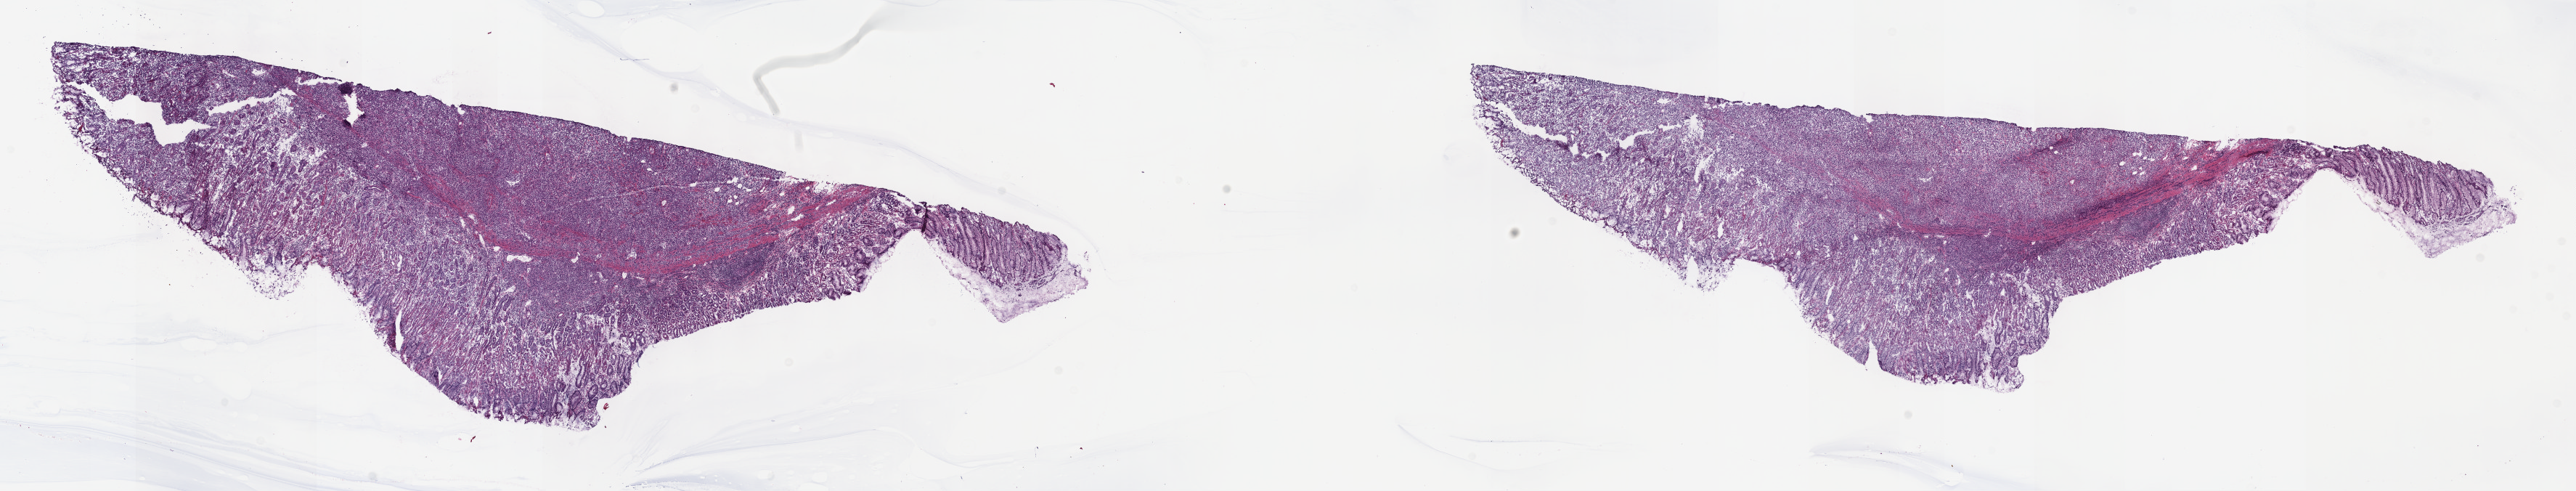
Hematoxylin and eosin (H&E) stained whole-slide image, shown as a low-resolution overview of the whole scanned area (about 28.7 x 5.5 mm), frozen section, lymphoid tissue, primary tumour sample. Male patient; age at initial diagnosis 55 years. Slide review estimates, as recorded: tumour cells 50%, tumour nuclei 60%, normal cells 40%, stromal cells 10%, necrosis 0%. Infiltration values recorded for this section: lymphocyte infiltration 90%, monocyte infiltration 5%, neutrophil infiltration 0%.
Pathologic diagnosis: Diffuse large B-cell lymphoma, NOS (stomach, NOS).